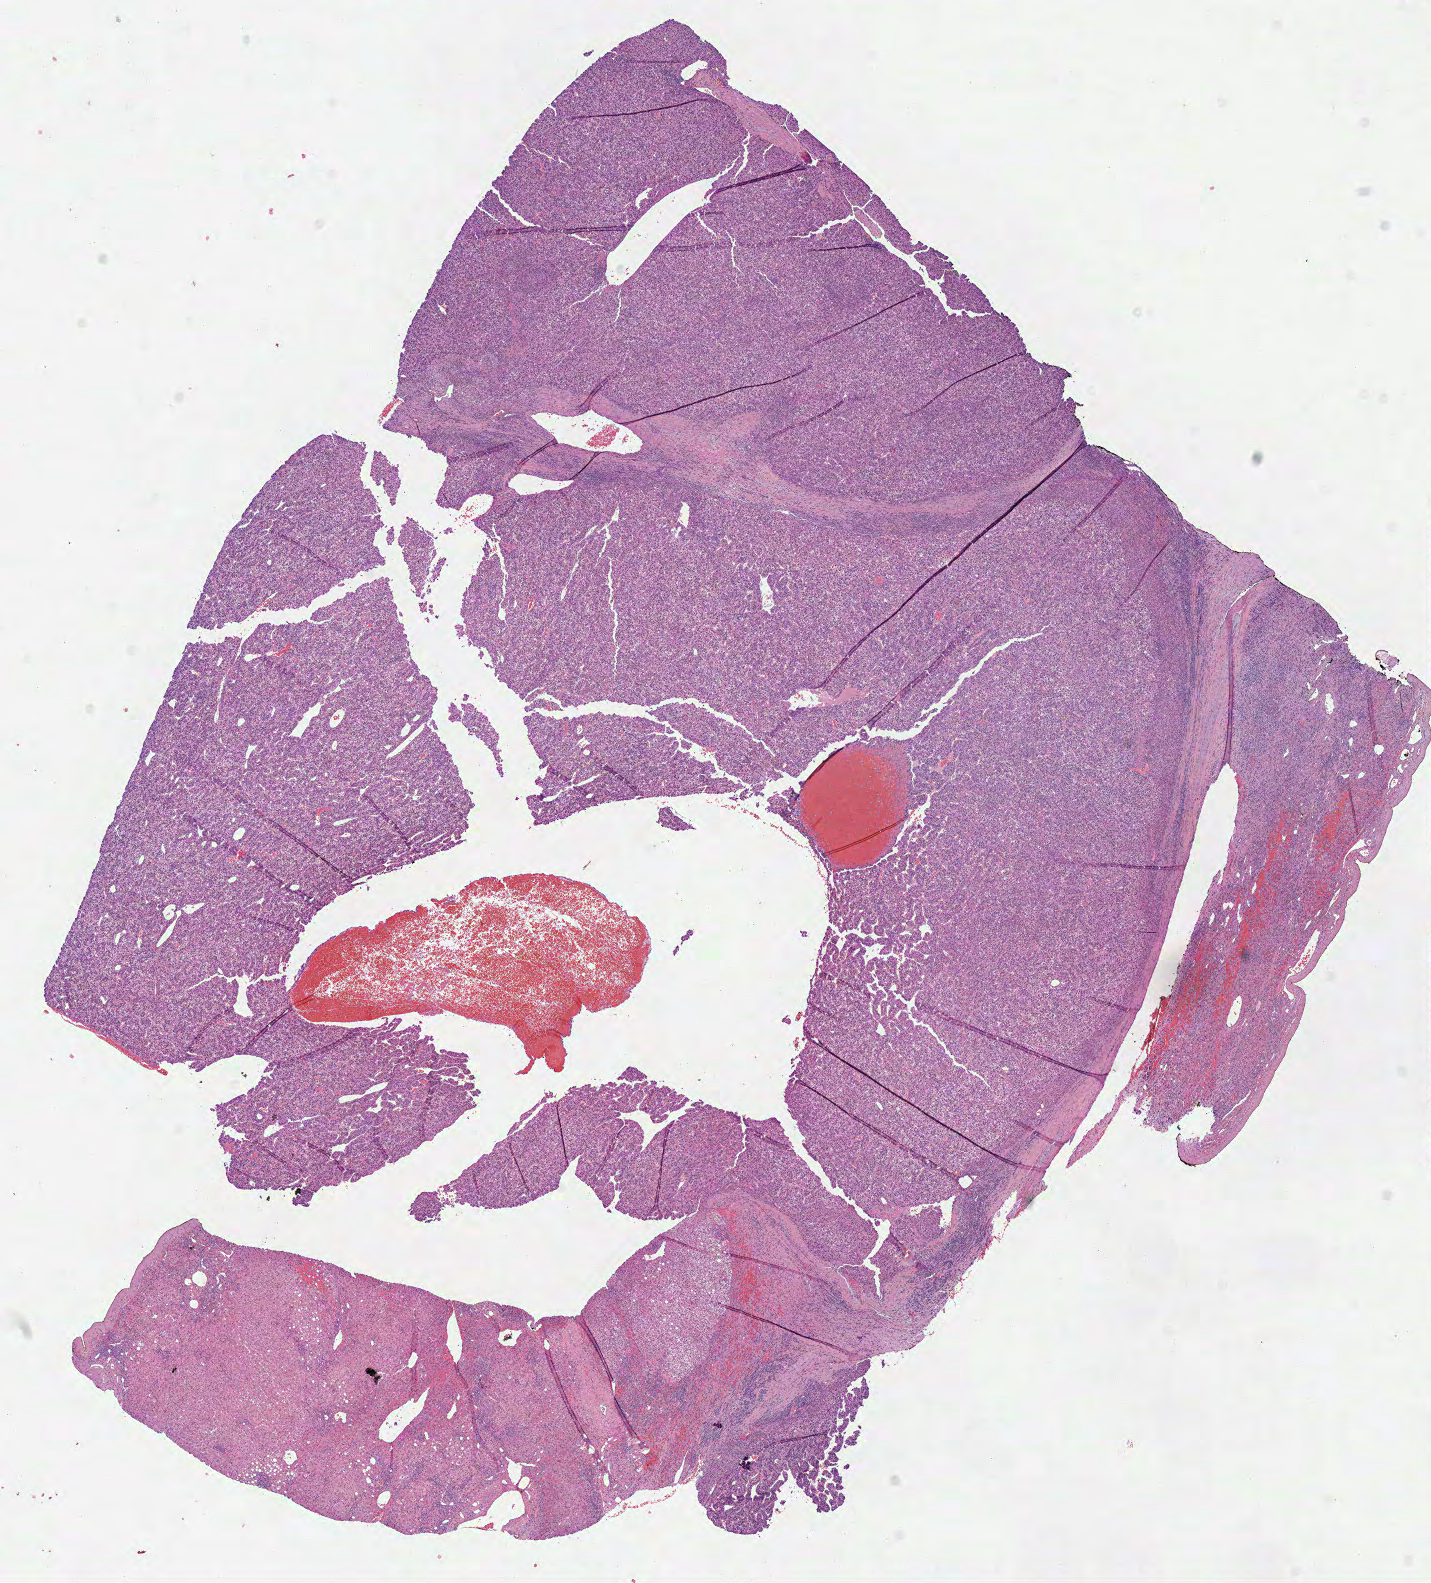
Whole-slide histology image, H&E-stained — low-resolution overview of the scanned area, about 11.3 x 12.5 mm. Formalin-fixed paraffin-embedded (FFPE) diagnostic section. Primary tumour sample from the liver. Female patient; age at initial diagnosis 70 years.
Pathologic diagnosis: Hepatocellular carcinoma, NOS. AJCC pathologic stage: II.